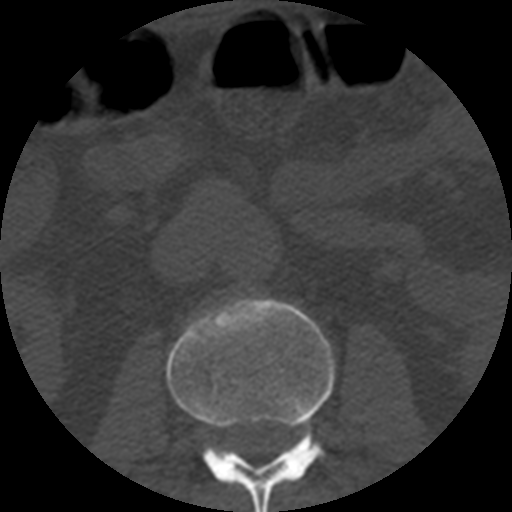
CT including the spine, one axial slice. Position 147 of 508 along the scan axis. 120 kVp. Bone window (W 1800 / L 400 HU). 1.25 mm slice thickness. 512 × 512 image matrix. Patient age 57 years. From the clinical record (not read from this slice): primary cancer: prostate.
Structures marked on this image (semi-automatically segmented with operator editing):
- L2 vertebra: bounding box (x1, y1, x2, y2) in pixels: (167, 298, 335, 512)